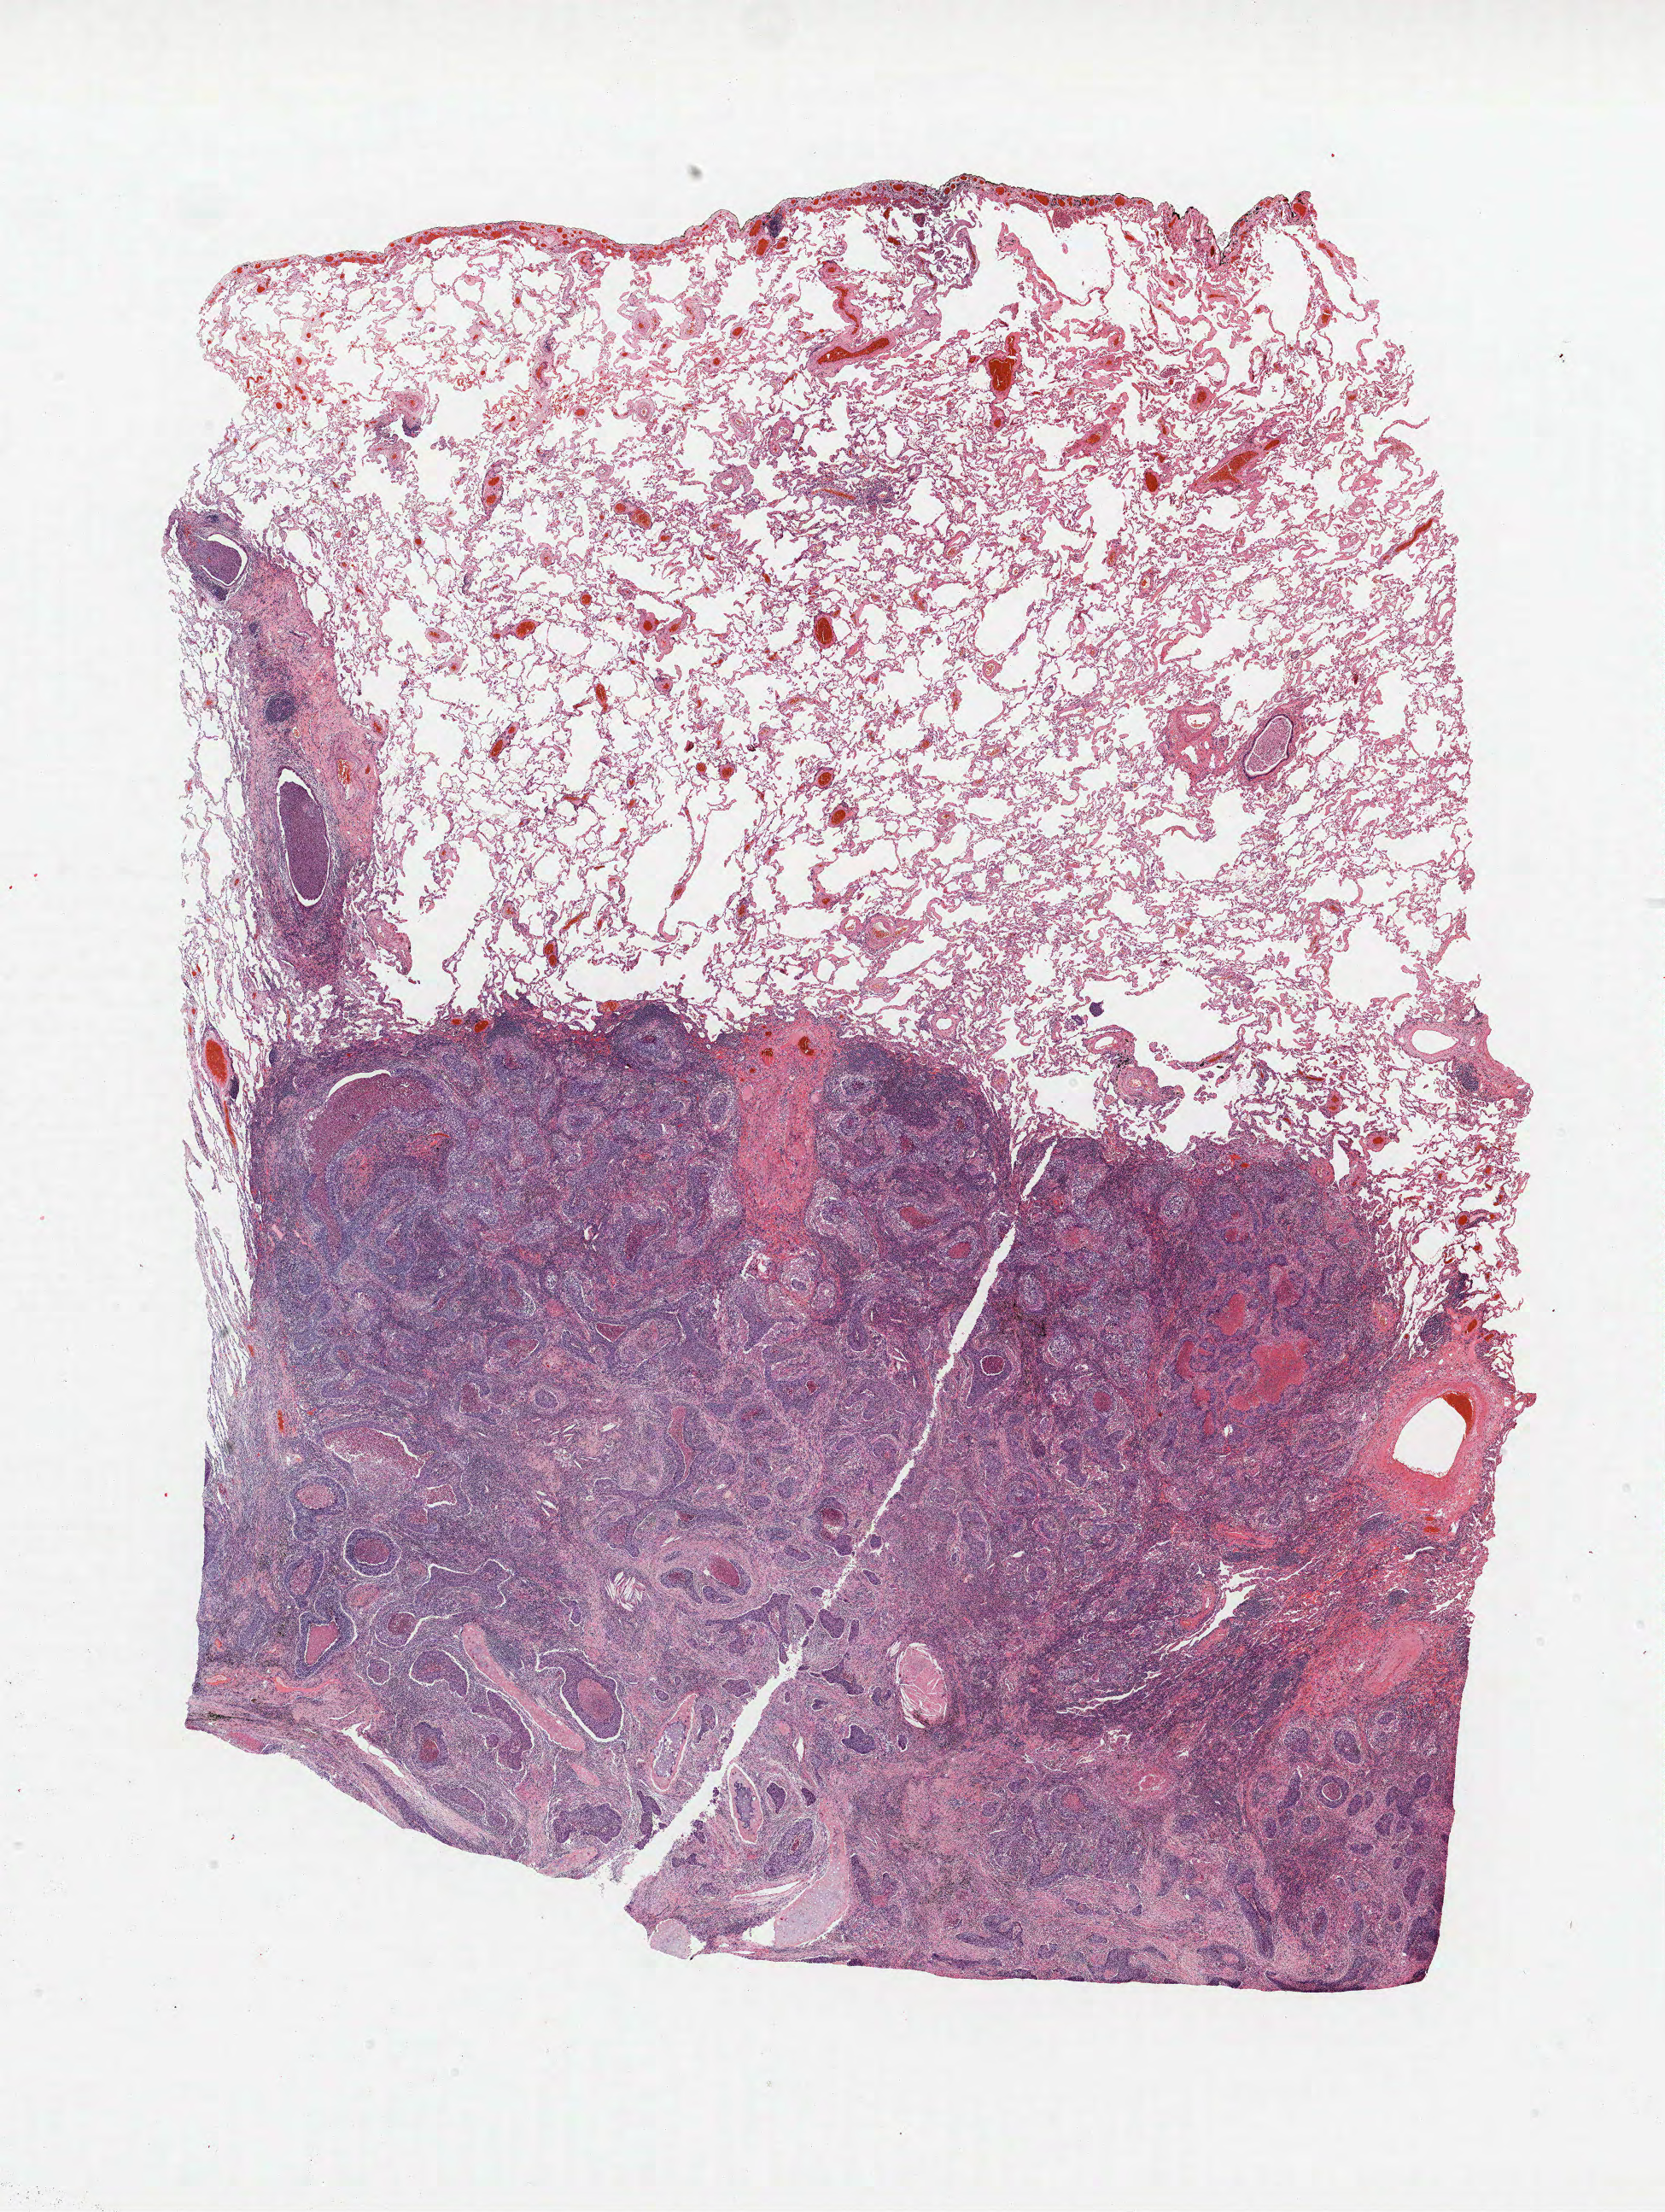
Whole-slide histology image, H&E, whole scanned area (about 15.6 x 20.7 mm, acquisition: 40x scan) shown as a low-resolution overview, FFPE section, lung. Female, age 67 at enrolment. Grade: poorly differentiated (G3).
- participant's lung-cancer diagnosis: Squamous cell carcinoma, NOS
- primary tumour location (clinical record): left lower lobe
- tumour size (pathology): 50 mm
- stage (AJCC 6th edition): IB